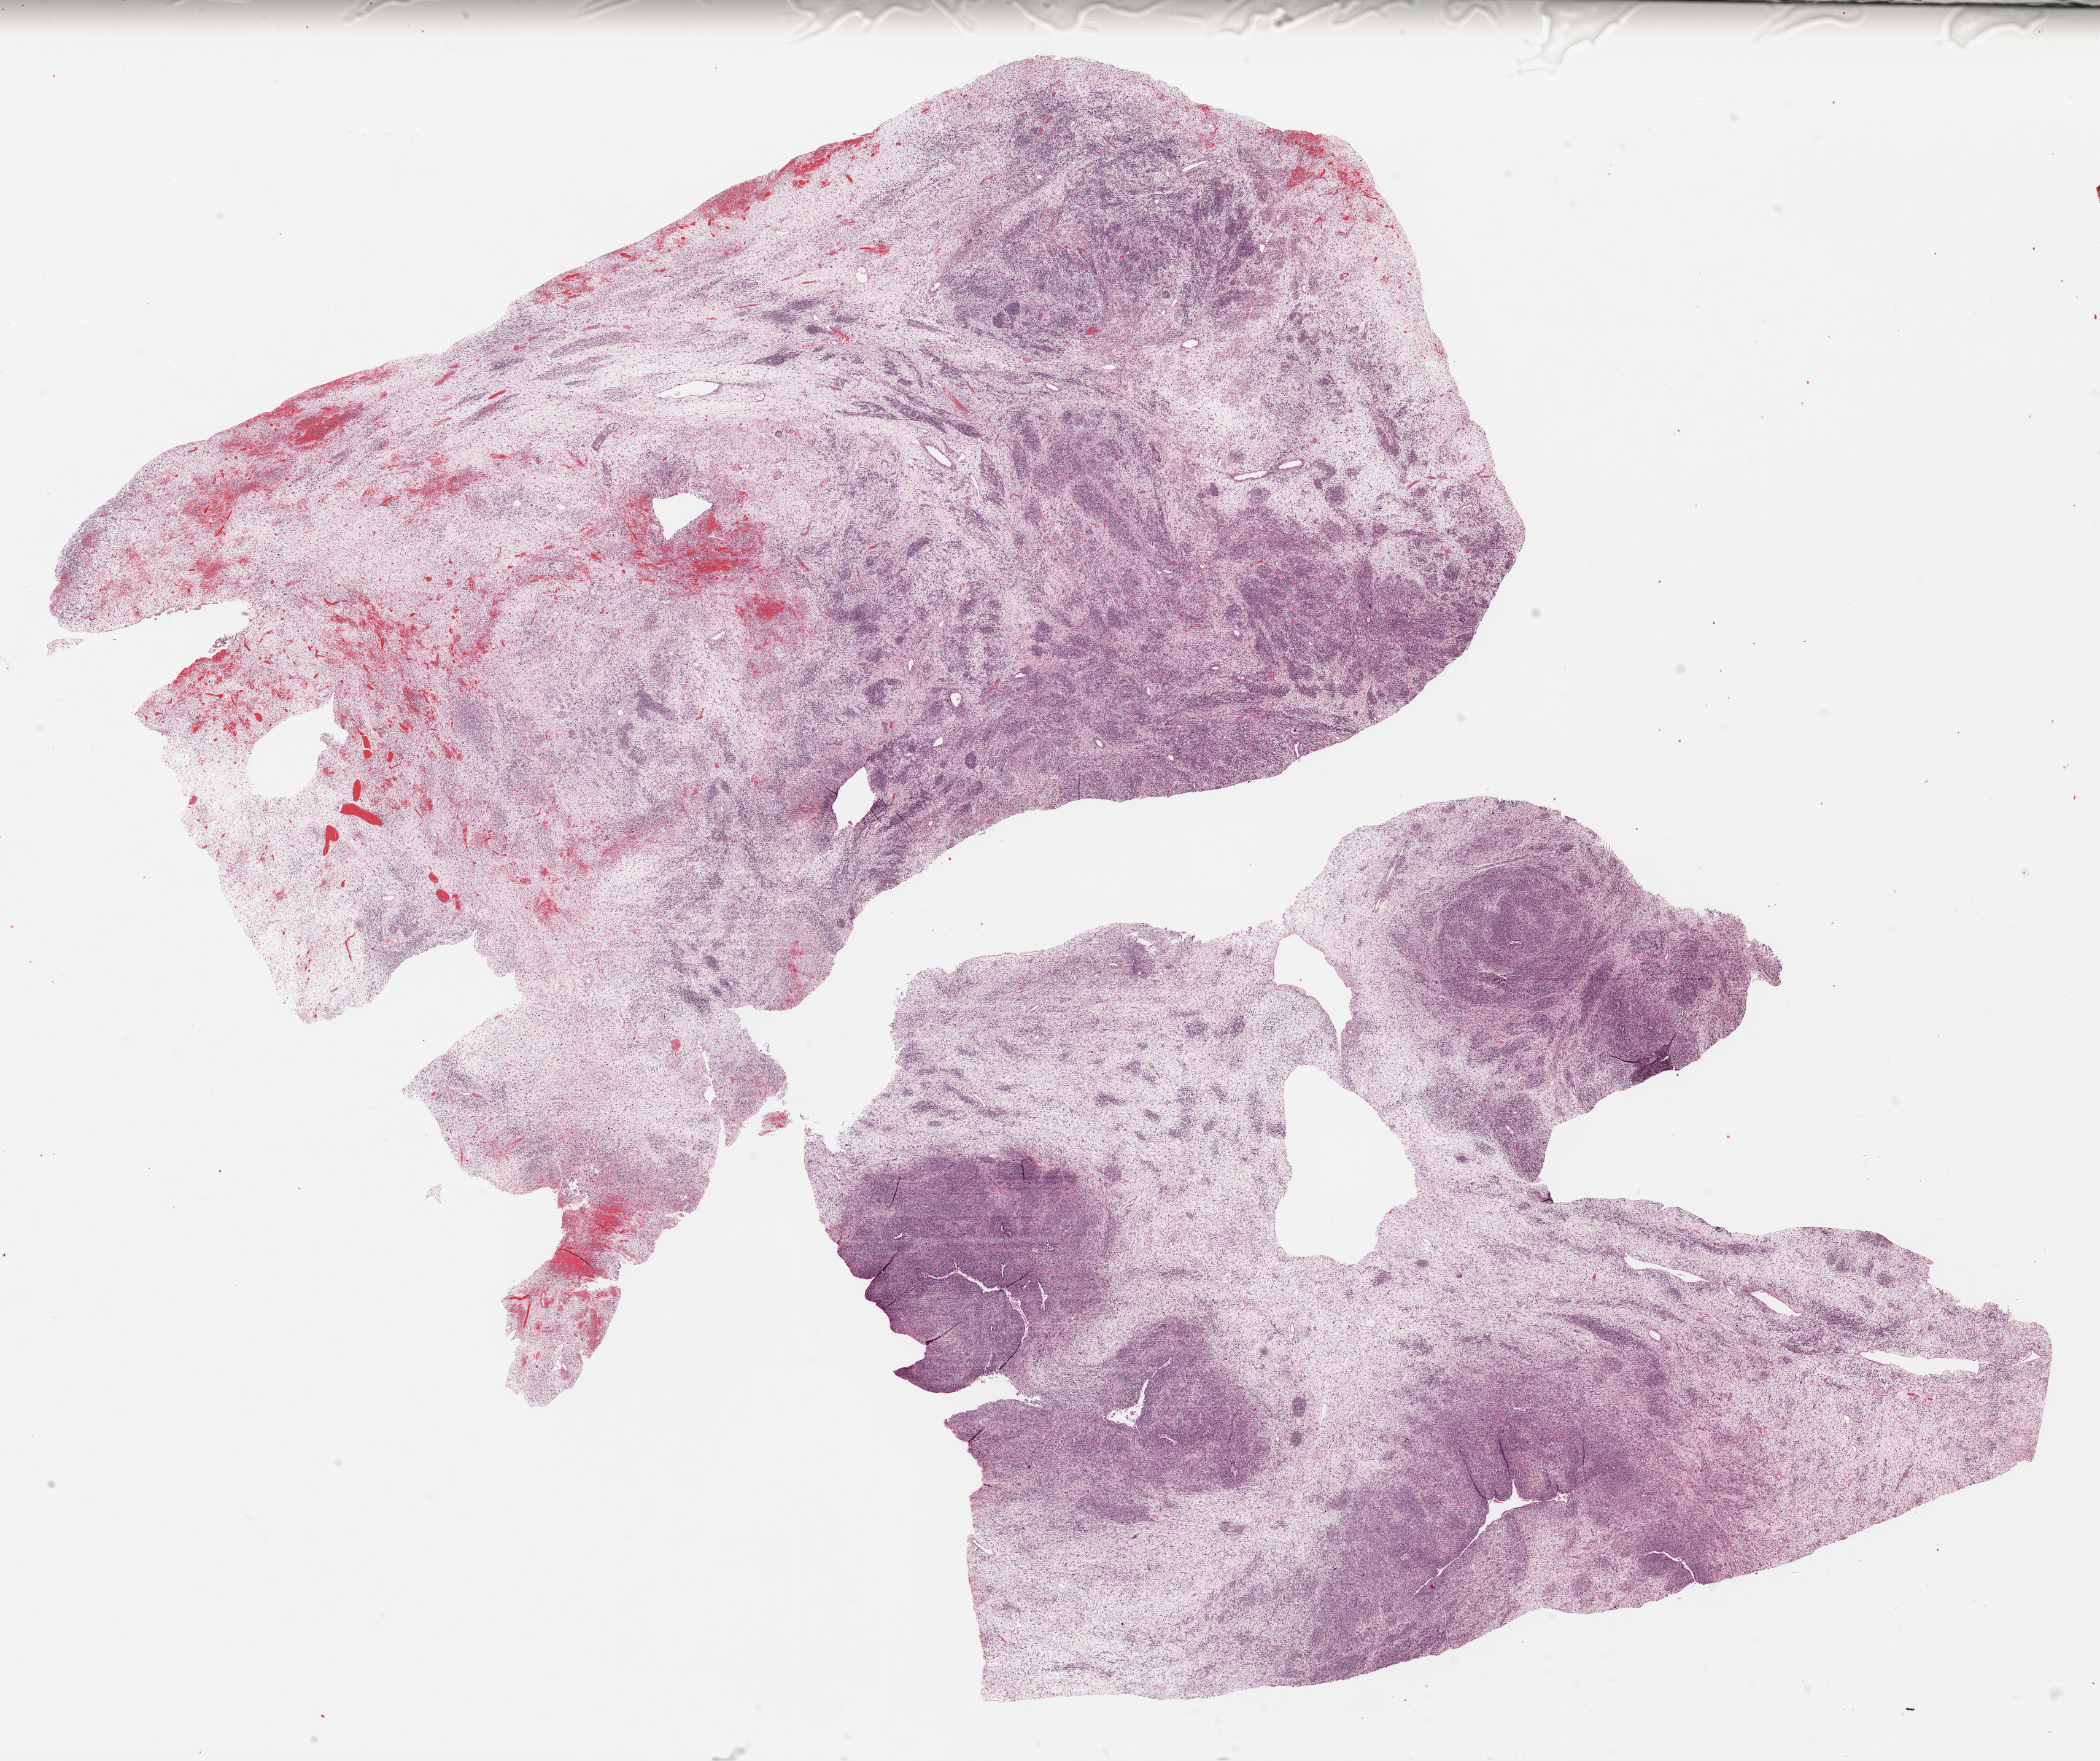
Whole-slide histology image, H&E, low-resolution overview of the scanned area, about 26.9 x 22.5 mm (from a 40x scan). Formalin-fixed paraffin-embedded (FFPE) diagnostic section. Primary tumour sample from the uterus. Female, age 68 years at initial diagnosis.
FIGO stage: IIIC1. Diagnosis: Carcinosarcoma, NOS (endometrium).